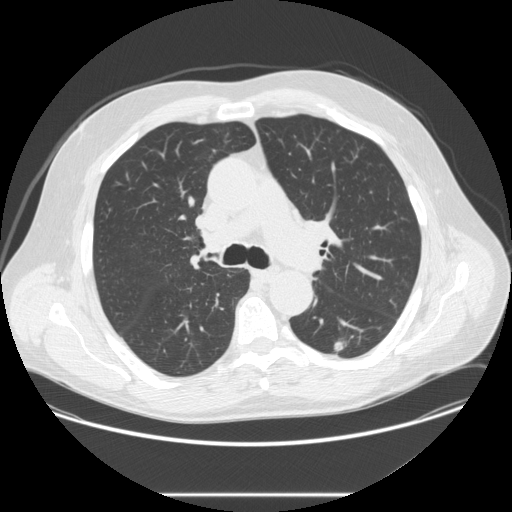
Low-dose screening chest CT, one axial slice. Slice 165 of 262 in the series (ordered by position). Reconstruction kernel STANDARD. Lung window (W 1500 / L -600 HU). 2.5 mm slice thickness. 512 × 512 image matrix.
Annotated regions visible in this slice (manually delineated by an expert):
- lesion 1 (tumor, lower lobe of left lung): bounding box <334,341,346,351> (left, top, right, bottom; pixels)